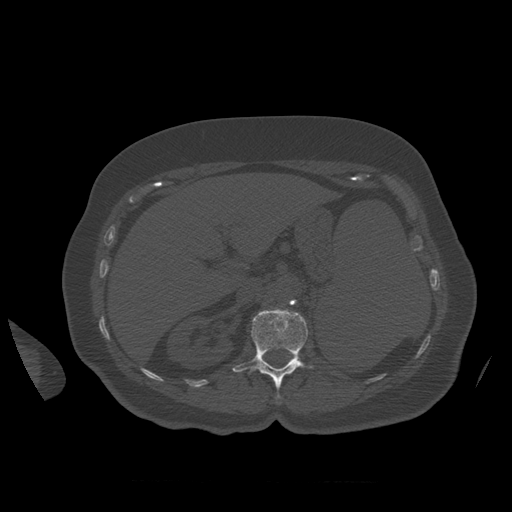
CT including the spine, one axial slice. Position 277 of 399 along the scan axis. Reconstruction kernel STANDARD. Bone window (W 1800 / L 400 HU). 512 × 512 image matrix, field of view 404 × 404 mm. Patient age 81 years. Case-level facts recorded for this patient, not image findings: primary cancer: renal; vertebrae with lytic lesions (as recorded): L1.
Annotated regions visible in this slice (semi-automatically segmented with operator editing):
- L1 vertebra: bounding box (x1, y1, x2, y2) in pixels: (233, 308, 313, 400)